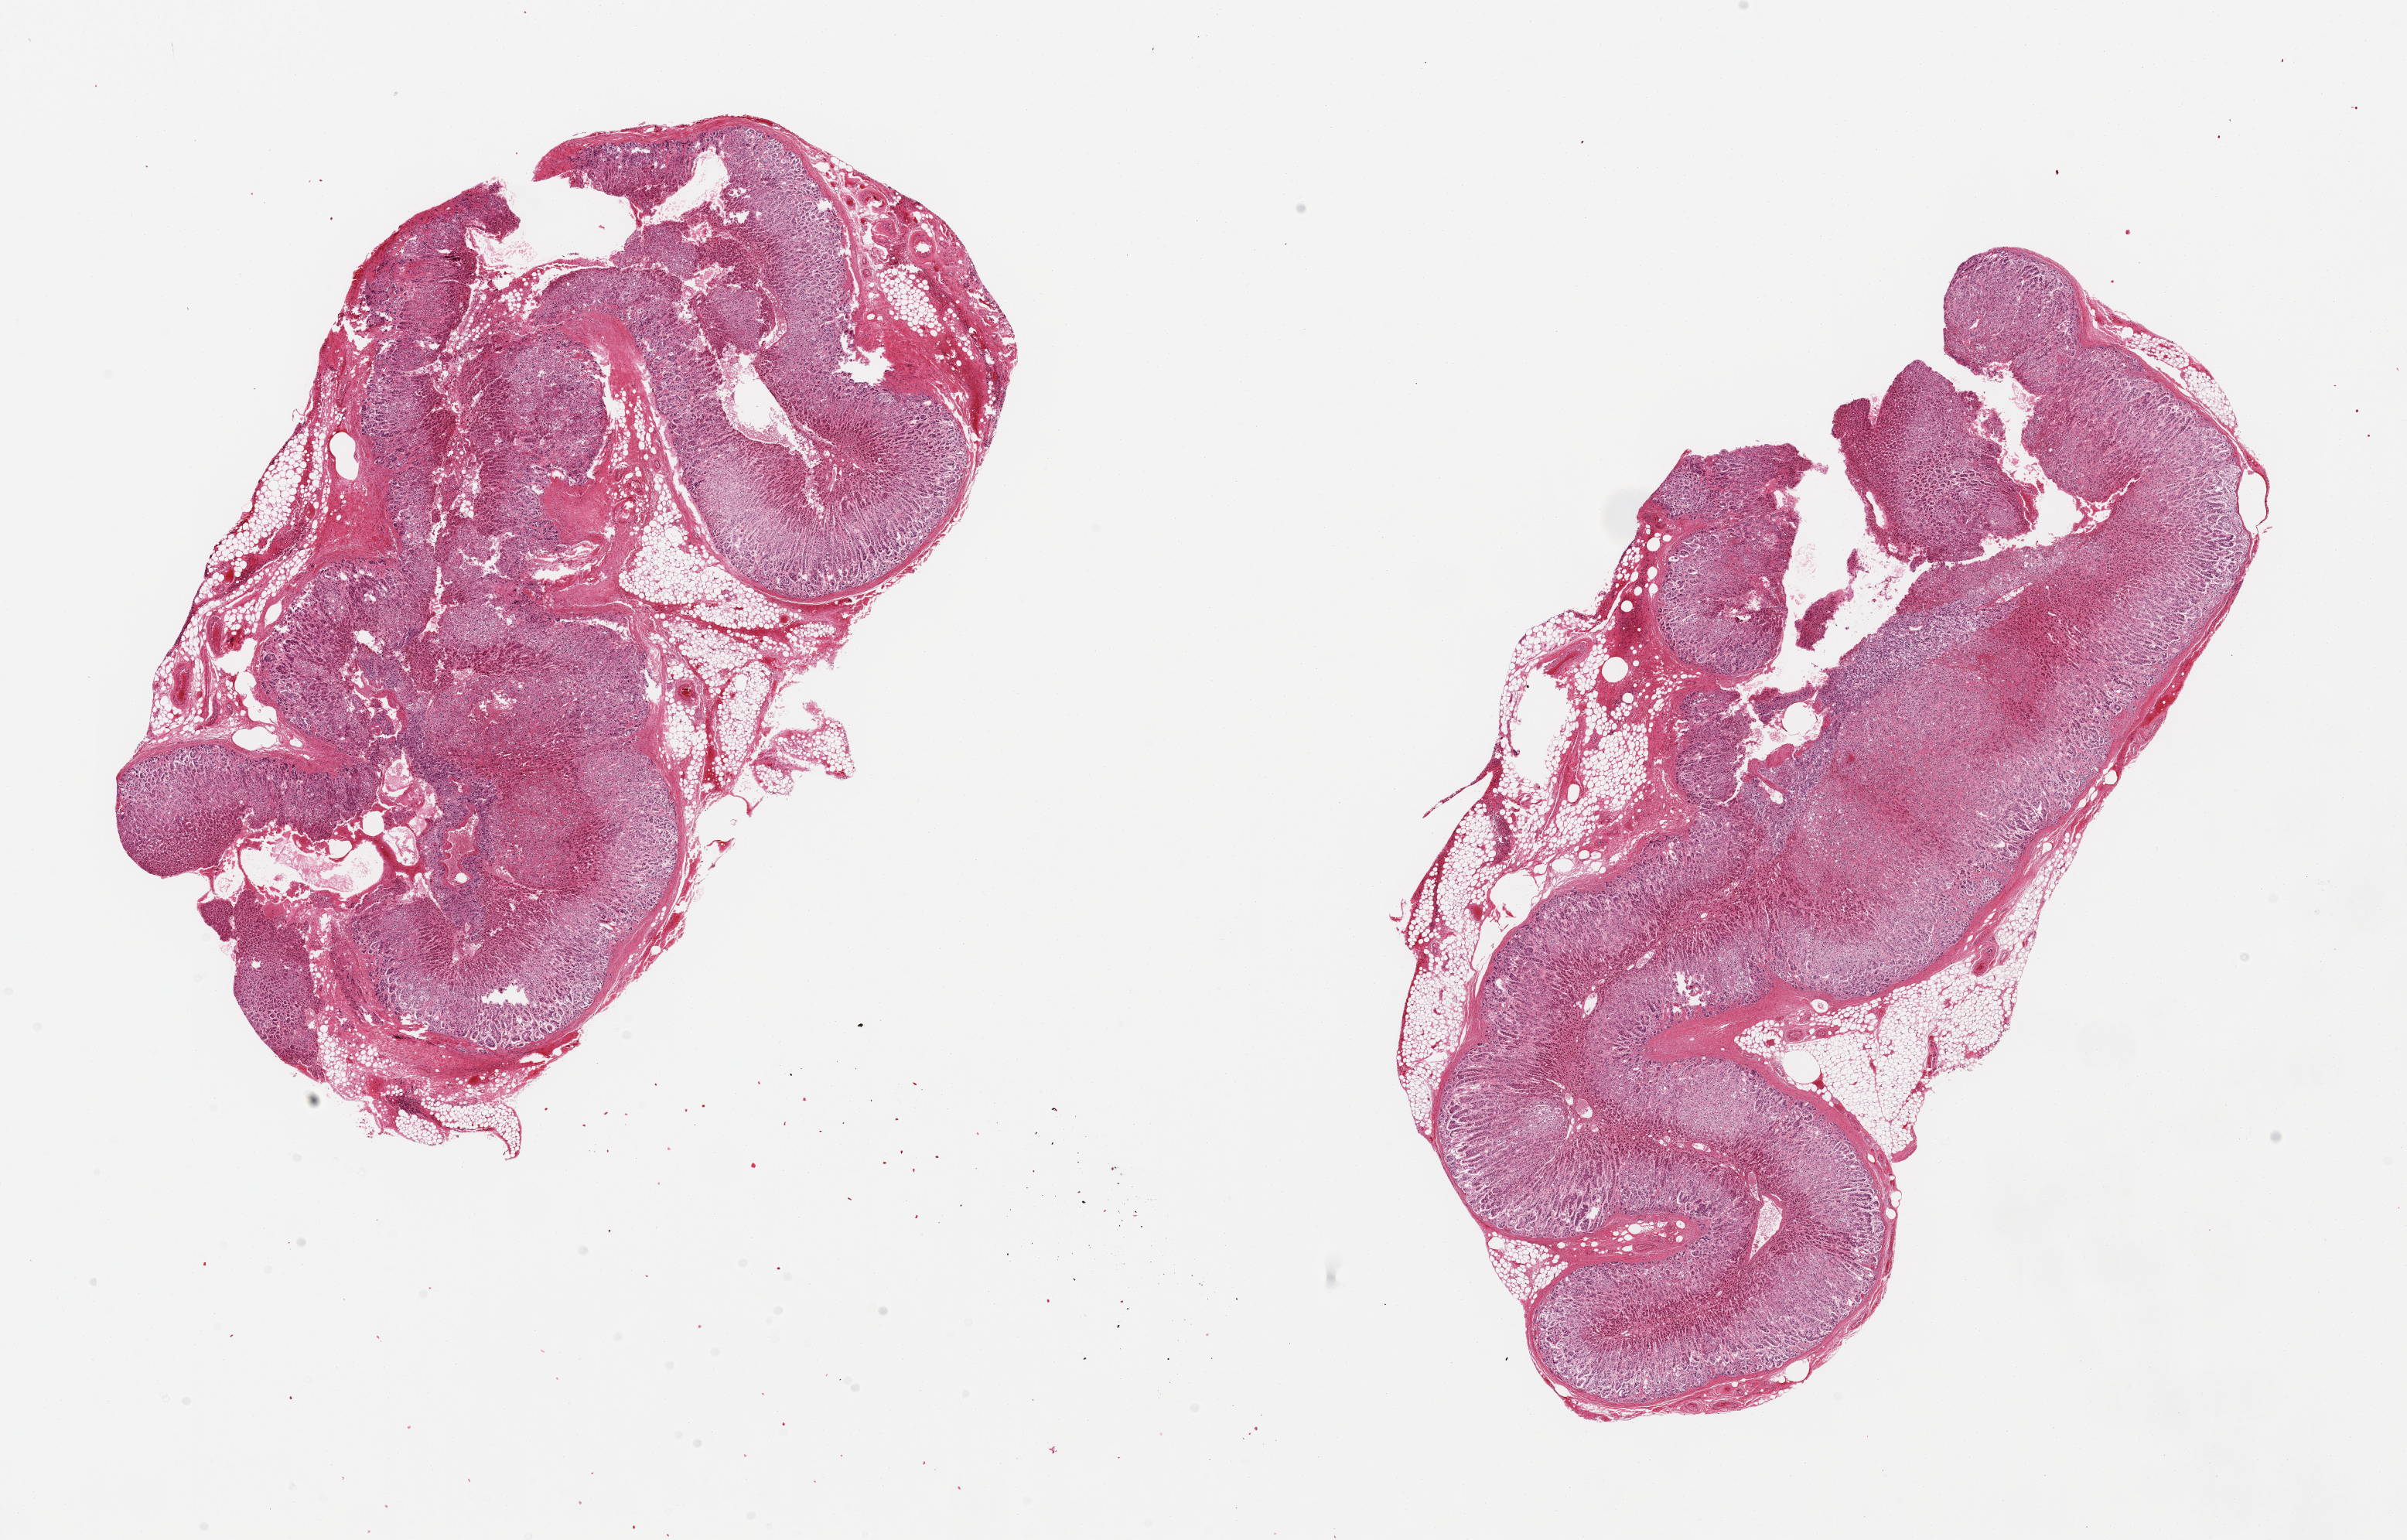
Whole-slide image, hematoxylin and eosin (H&E) stain — a low-resolution overview of the entire scanned area, about 24.6 x 15.7 mm. PAXgene-fixed, paraffin-embedded tissue. Target tissue: adrenal gland. Donor tissue sample. Donor: female.
• reviewer comment on this tissue sample: 2 pieces, 12x6 & 11x6 mm; 10-20% adipose